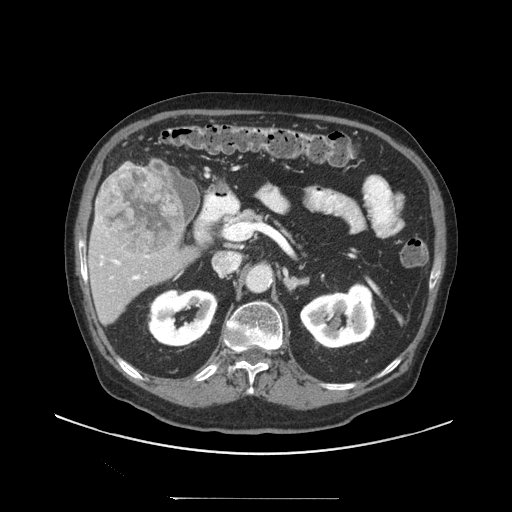
Contrast-enhanced abdominal CT (liver protocol), one axial slice. Position 50 of 97 along the scan axis. Reconstruction kernel STANDARD. 140 kVp. Soft-tissue window (W 400 / L 40 HU). 2.5 mm slice thickness. 512 × 512 image matrix, field of view 450 × 450 mm. Case-level facts recorded for this patient, not image findings: diagnosis: hepatocellular carcinoma (patient treated with transarterial chemoembolisation; whether this scan precedes or follows treatment is not stated here); TNM stage (as recorded): Stage-IIIC; Child-Pugh class: A; tumour nodularity: uninodular; tumour size: 9.2 cm.
Annotated regions visible in this slice (semi-automatic segmentation, software-assisted and operator-edited):
- liver parenchyma outside the tumour (the mass and vessels are separate outlines, so this box may not span the whole liver): bounding box (x1, y1, x2, y2) in pixels: (90, 162, 197, 324)
- mass: (99, 167, 185, 258)
- liver vessels: (95, 166, 140, 280)